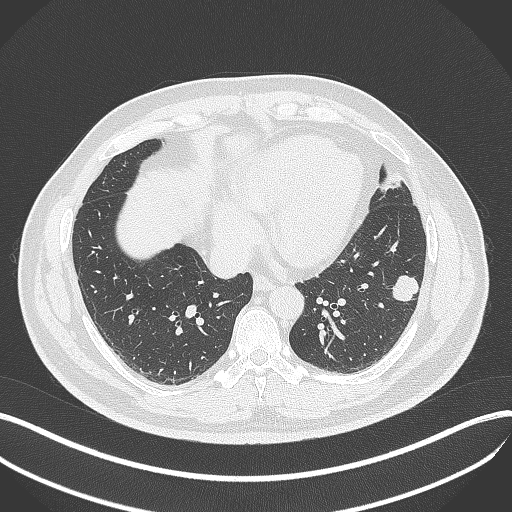
Chest CT, one axial slice. Slice 147 of 429 in the series (ordered by position). 120 kVp. Lung window (W 1500 / L -600 HU). 1 mm slice thickness. 512 × 512 image matrix, field of view 400 × 400 mm. Patient: male, 39 years. From the clinical record (not read from this slice): clinical TNM (as recorded): T2a N0 M0.
Annotated regions visible in this slice (bounding box drawn by a radiologist):
- lung tumour (recorded histology: adenocarcinoma): bounding box <388,271,422,308> (left, top, right, bottom; pixels)